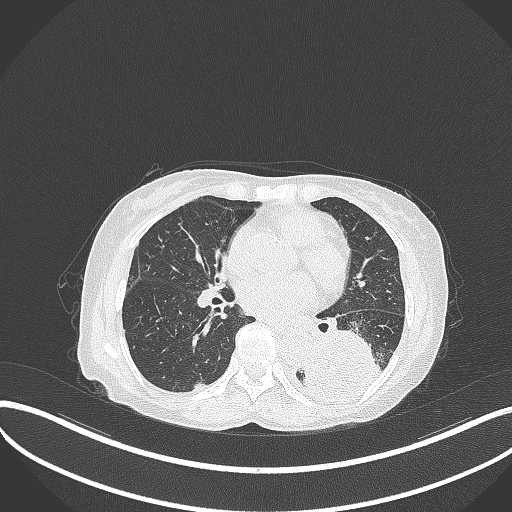
Chest CT, one axial slice; slice 143 of 370 in the series (ordered by position); reconstruction kernel B70f; 120 kVp; lung window (W 1500 / L -600 HU); 1 mm slice thickness; 512 × 512 image matrix, field of view 400 × 400 mm. Female patient, age 78 years. From the clinical record (not read from this slice): clinical TNM (as recorded): T3 N0 M1.
Annotated regions visible in this slice (bounding box drawn by a radiologist):
- lung tumour (recorded histology: squamous cell carcinoma): bounding box <298,322,386,404> (left, top, right, bottom; pixels)